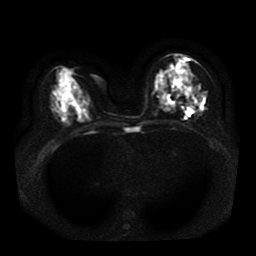
Breast MRI, one axial slice. Position 16 of 41 along the scan axis. Diffusion-weighted series; image 2 of 4 stored at this slice position (different b-values; order by instance number). 1.5 T. 5 mm slice thickness. 256 × 256 image matrix, field of view 330 × 330 mm. Female patient.
Annotated regions visible in this slice (expert manual segmentation):
- tumour on diffusion-weighted imaging: box from (x=176, y=71) to (x=202, y=110) px